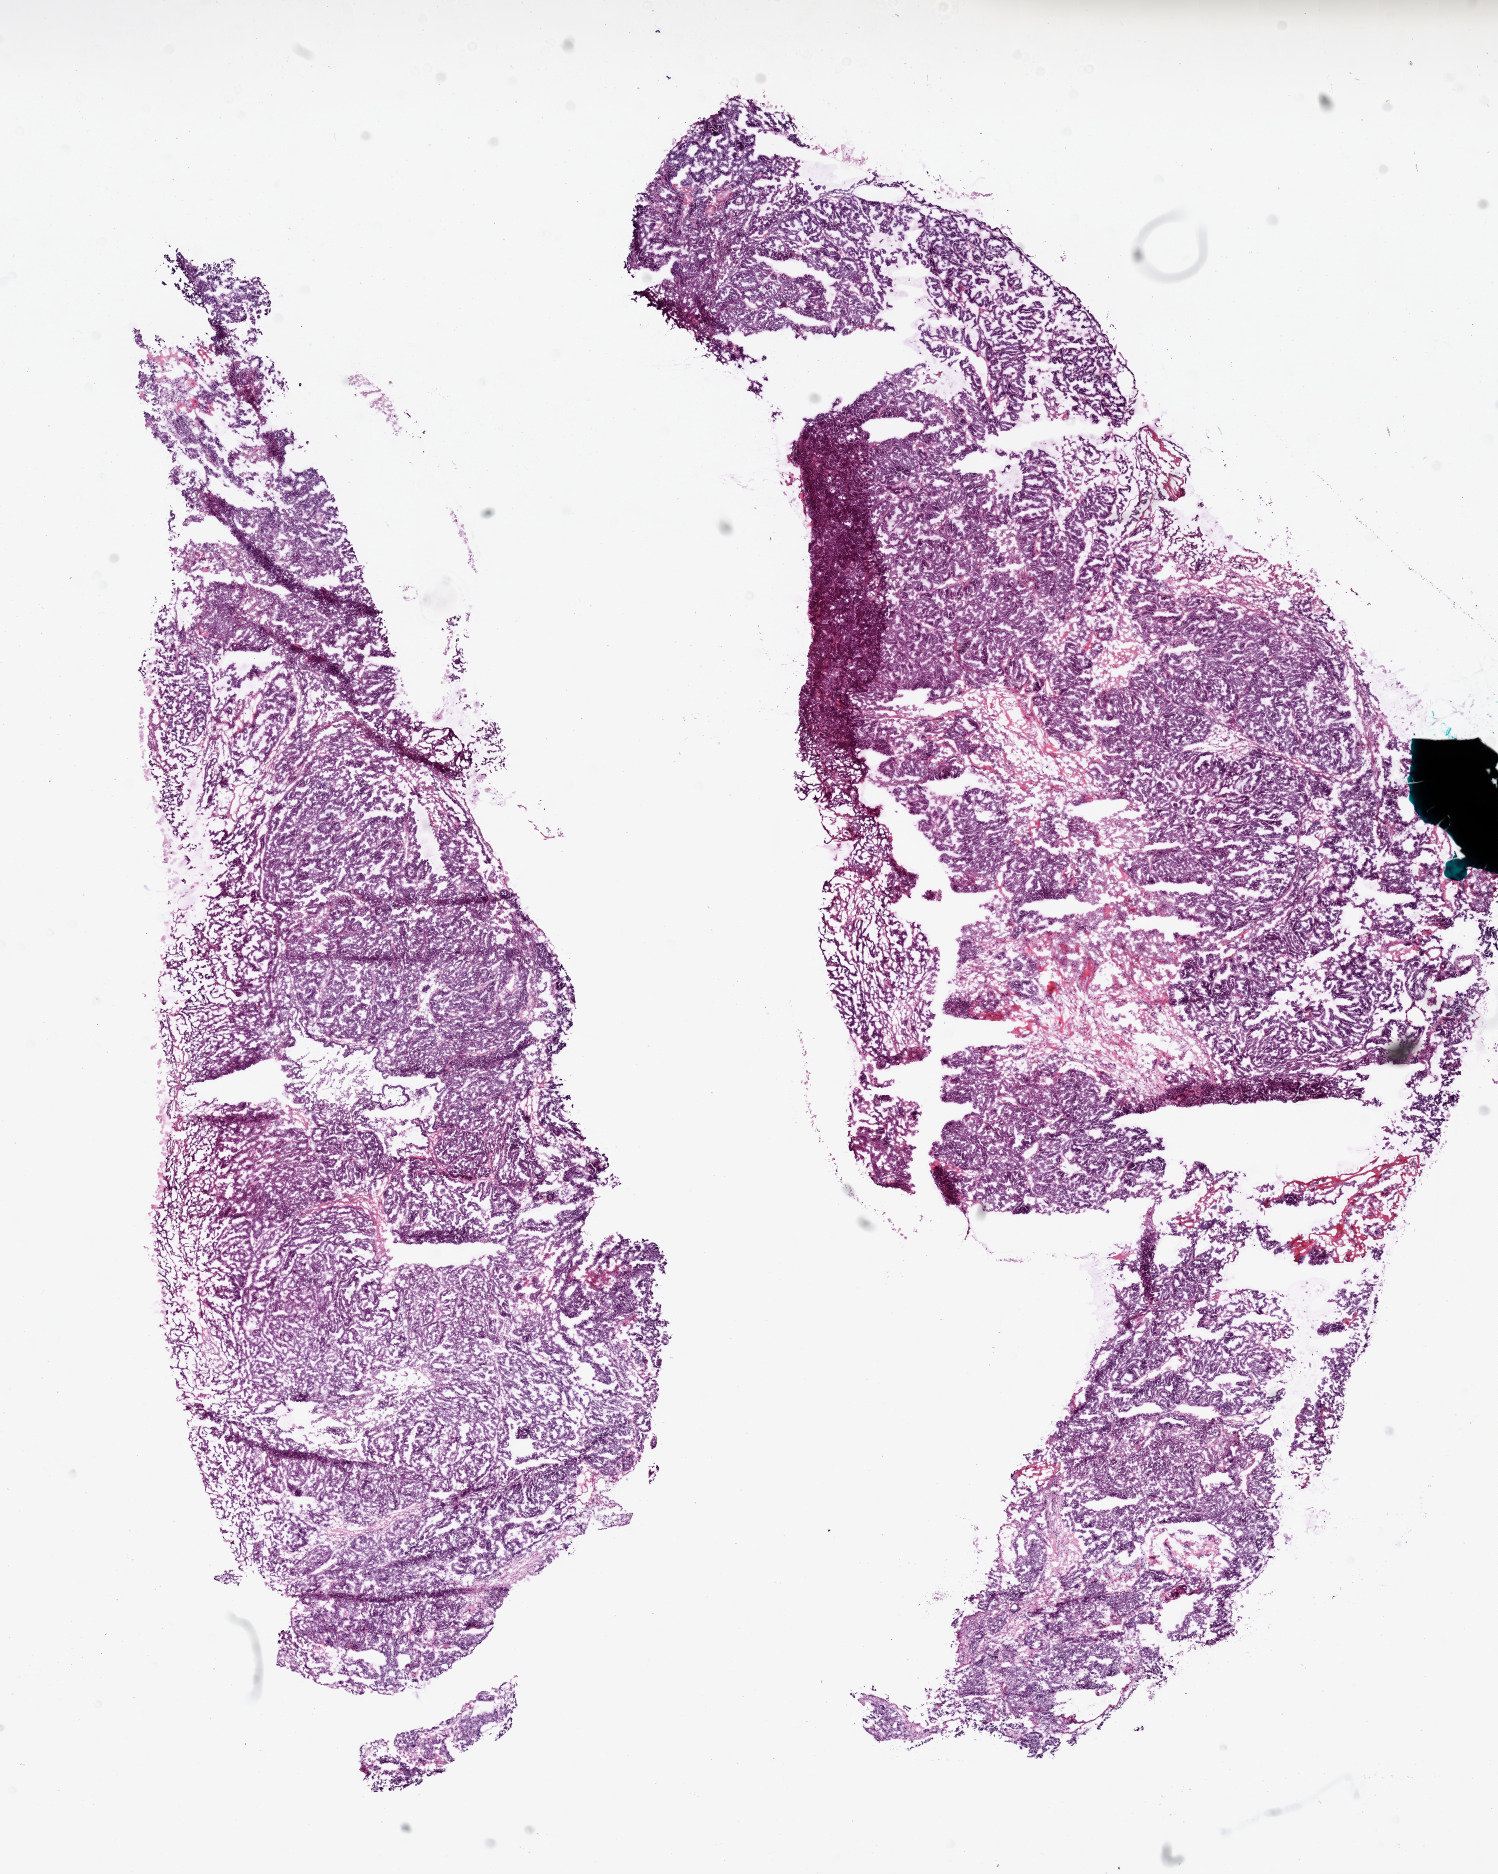
Whole-slide histology image, H&E-stained — shown as a low-resolution overview of the whole scanned area (about 12.1 x 15.1 mm, from a 20x scan). Frozen section. Primary tumour sample from the ovary. Female patient; age at initial diagnosis 53 years. Histologic grade: G2 (moderately differentiated). Pathologist review of this section (percent, as recorded): tumour cells 85%, tumour nuclei 90%, normal cells 0%, stromal cells 10%, necrosis 5%.
FIGO stage: IIIC. Diagnosis: Serous cystadenocarcinoma, NOS.